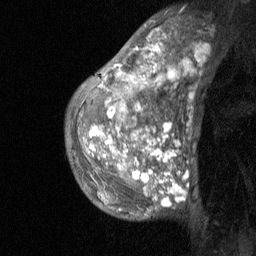
Breast MRI (dynamic contrast-enhanced), one sagittal slice; position 43 of 64 along the scan axis; dynamic contrast-enhanced study with each time point stored as its own series, time point 2 of 3 at this slice position (early post-contrast, ordered by acquisition time); 1.5 T; TE 4.8 ms, TR 27 ms; 256 × 256 image matrix, field of view 180 × 180 mm. Female patient, age 36 years. From the clinical record (not read from this slice): setting: breast cancer imaged before/during neoadjuvant chemotherapy; receptor status: HR-positive, HER2-negative.
Outlined on this slice (semi-automatically segmented with operator editing):
- analysis volume of interest (the breast-tissue region the enhancement analysis was run in; not a lesion): bounding box (x1, y1, x2, y2) in pixels: (67, 14, 201, 221)
- tumour enhancement mask (voxels above the 90 % enhancement threshold inside the analysis volume of interest): (90, 44, 175, 204)